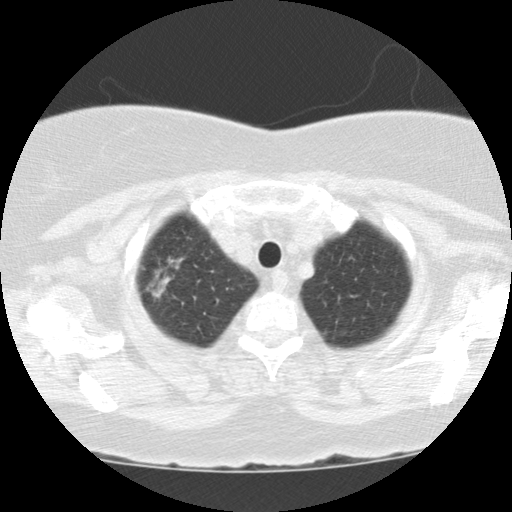
Axial slice from a low-dose chest CT screening exam; first (baseline) screen; lung window (W 1500 / L -600 HU); slice 11 of 112 in the series. Female, age 67 years at enrolment. Former smoker at enrolment.
Expert reader's lesion annotation, box from (x=132, y=244) to (x=198, y=307) px. The screening reader recorded 3 non-calcified nodules or masses ≥4 mm on this exam (right upper lobe, right lower lobe, right upper lobe); which of them this box marks is not recorded. Lung cancer was diagnosed 441 days after this screen (after the second annual screen): adenocarcinoma with mixed subtypes, right upper lobe, poorly differentiated (G3), stage IA (AJCC 6th edition), 30 mm at pathology.